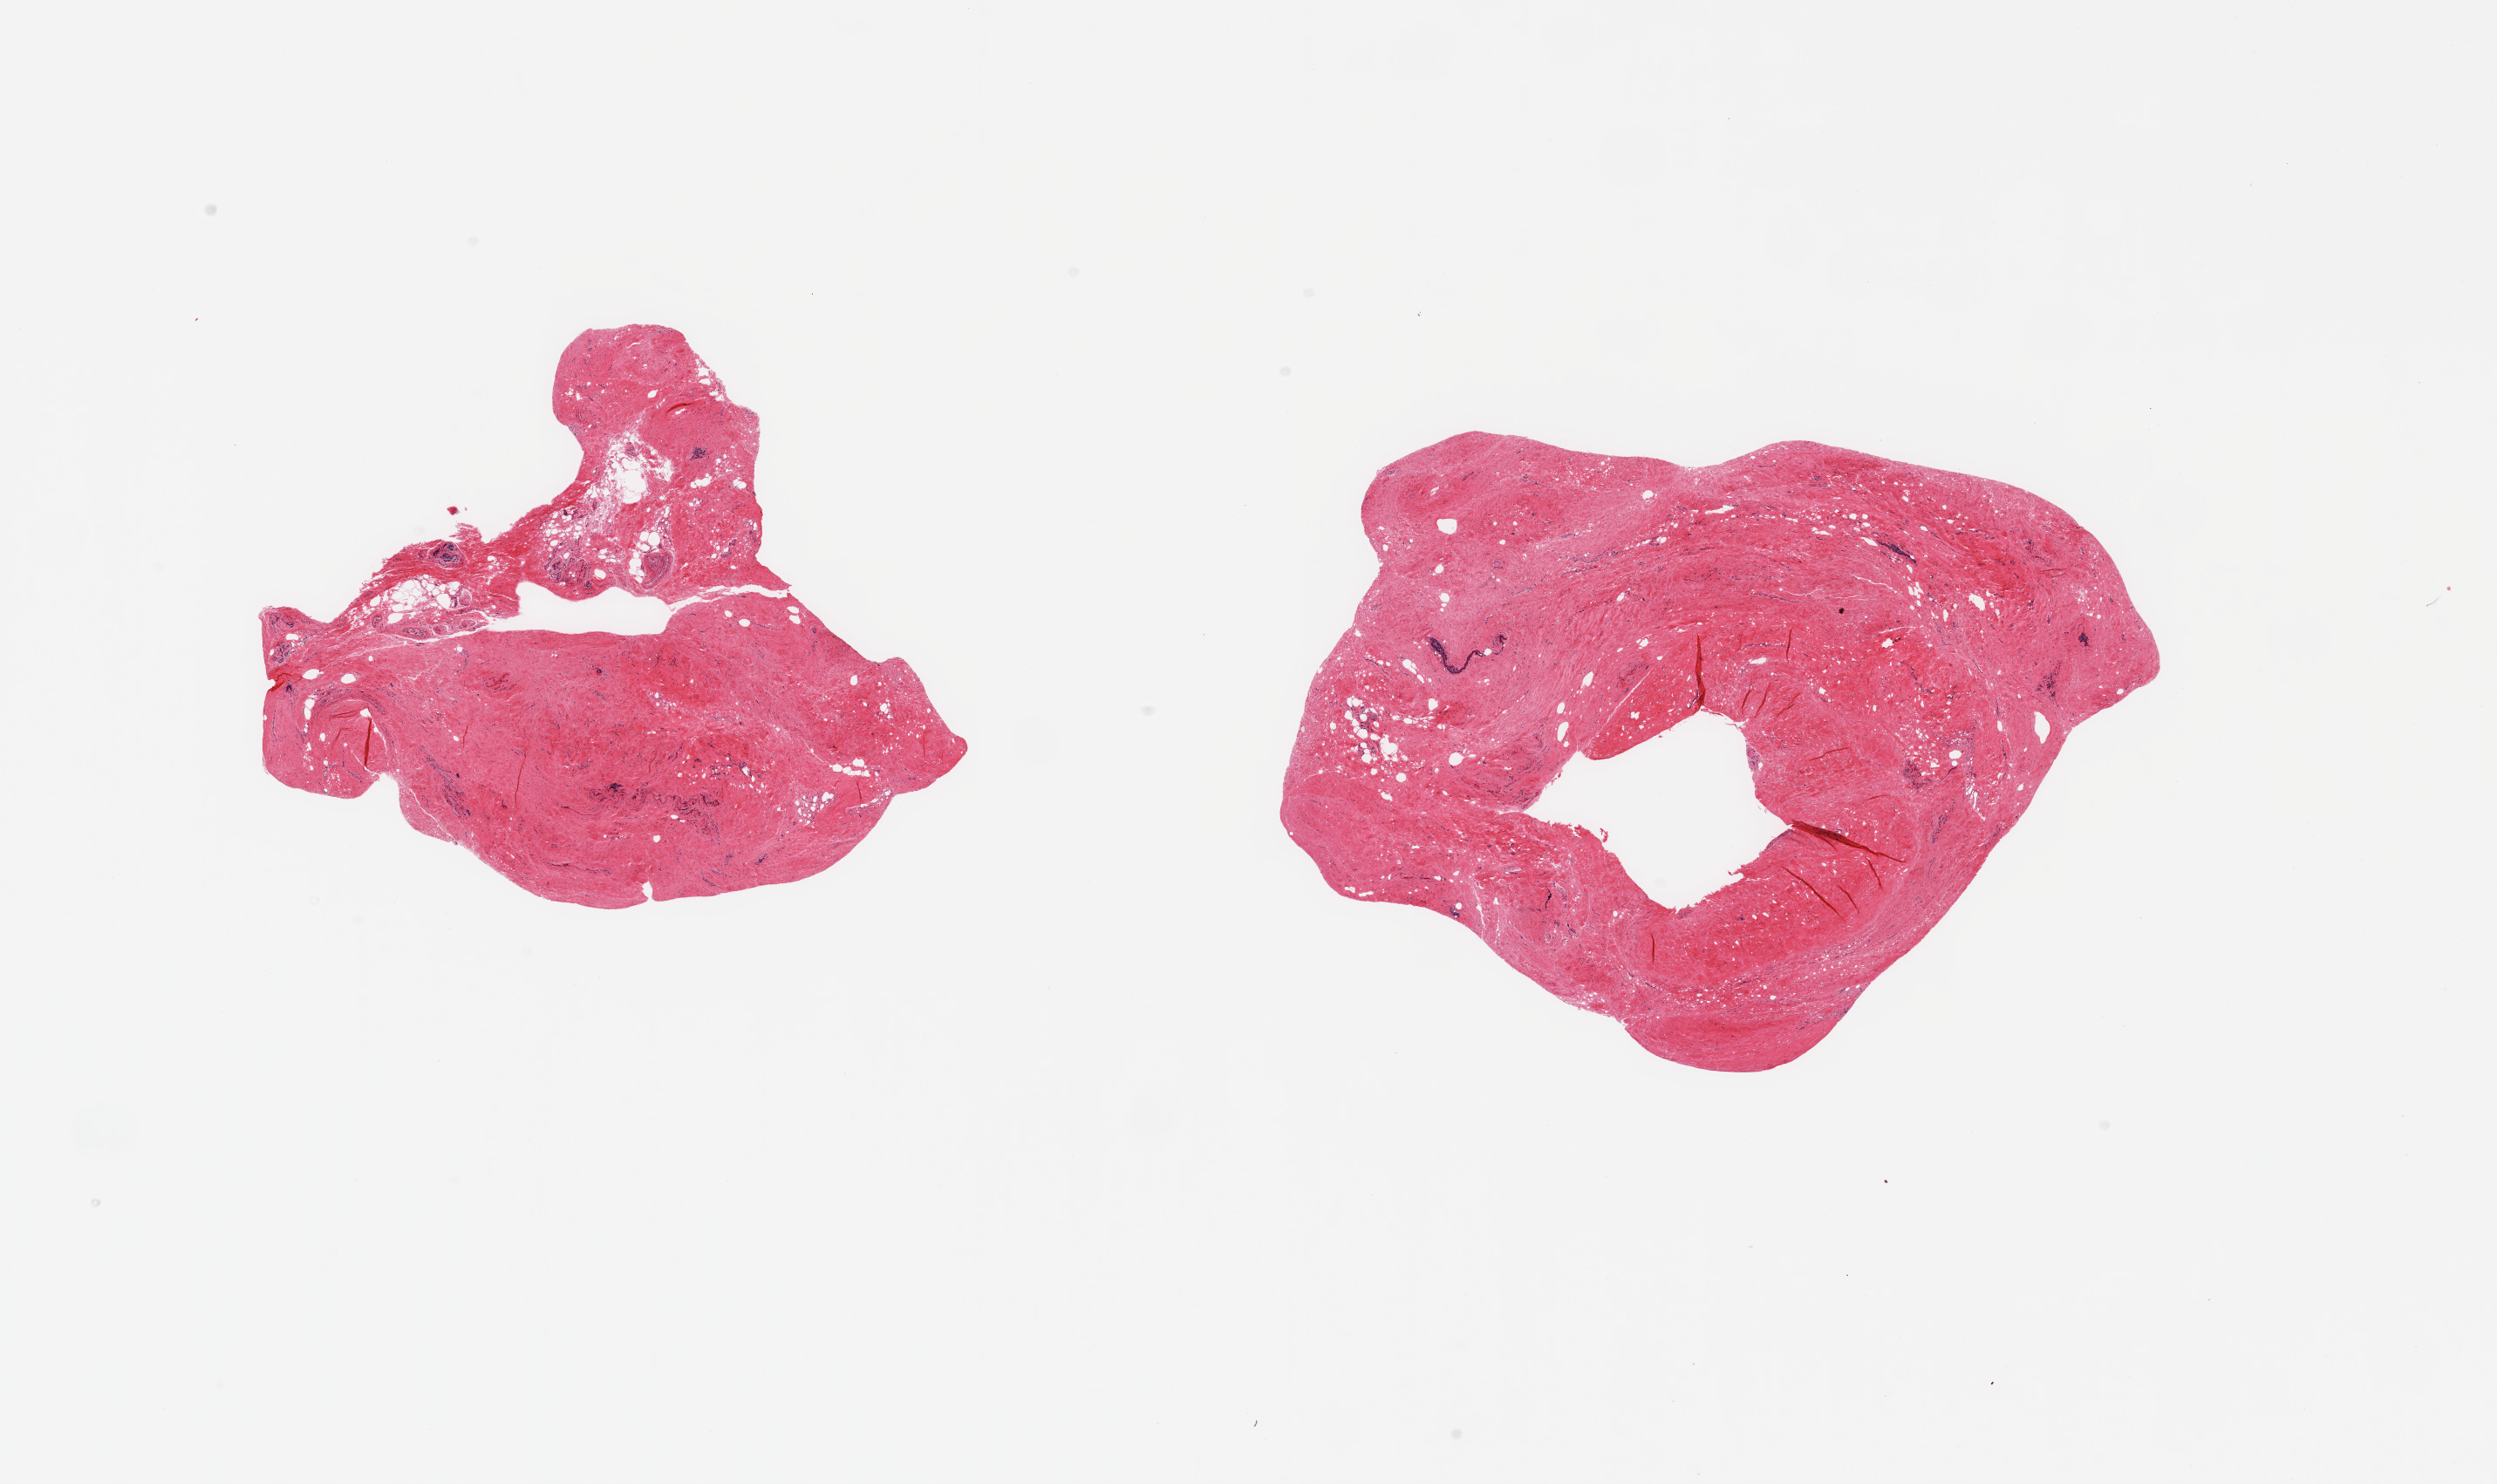
H&E whole-slide image, brightfield — whole scanned area (about 22.6 x 13.5 mm, from a 20x scan) shown as a low-resolution overview. PAXgene-fixed, paraffin-embedded tissue. Sampled site (target tissue): breast. Donor tissue sample. Donor: male.
Review note (as recorded): 2 pieces, gynecomastoid stromal hyperplasia, focal ductal elements noted.